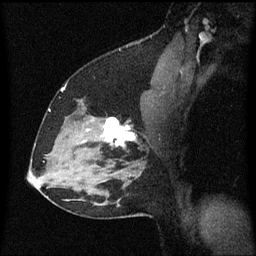
Breast MRI (dynamic contrast-enhanced), one sagittal slice. Position 41 of 60 along the scan axis. Dynamic contrast-enhanced series, image 2 of 3 at this slice position (ordered by acquisition). 1.5 T. TE 4.2 ms, TR 8.4 ms. 256 × 256 image matrix, field of view 200 × 200 mm. Patient: female, 37 years. From the clinical record (not read from this slice): setting: breast cancer imaged before/during neoadjuvant chemotherapy; receptor status: HR-positive, HER2-negative.
Structures marked on this image (semi-automatically segmented with operator editing):
- analysis volume of interest (the breast-tissue region the enhancement analysis was run in; not a lesion): bounding box <94,118,141,157> (left, top, right, bottom; pixels)
- tumour enhancement mask (voxels above the 70 % enhancement threshold inside the analysis volume of interest): <104,118,135,147>